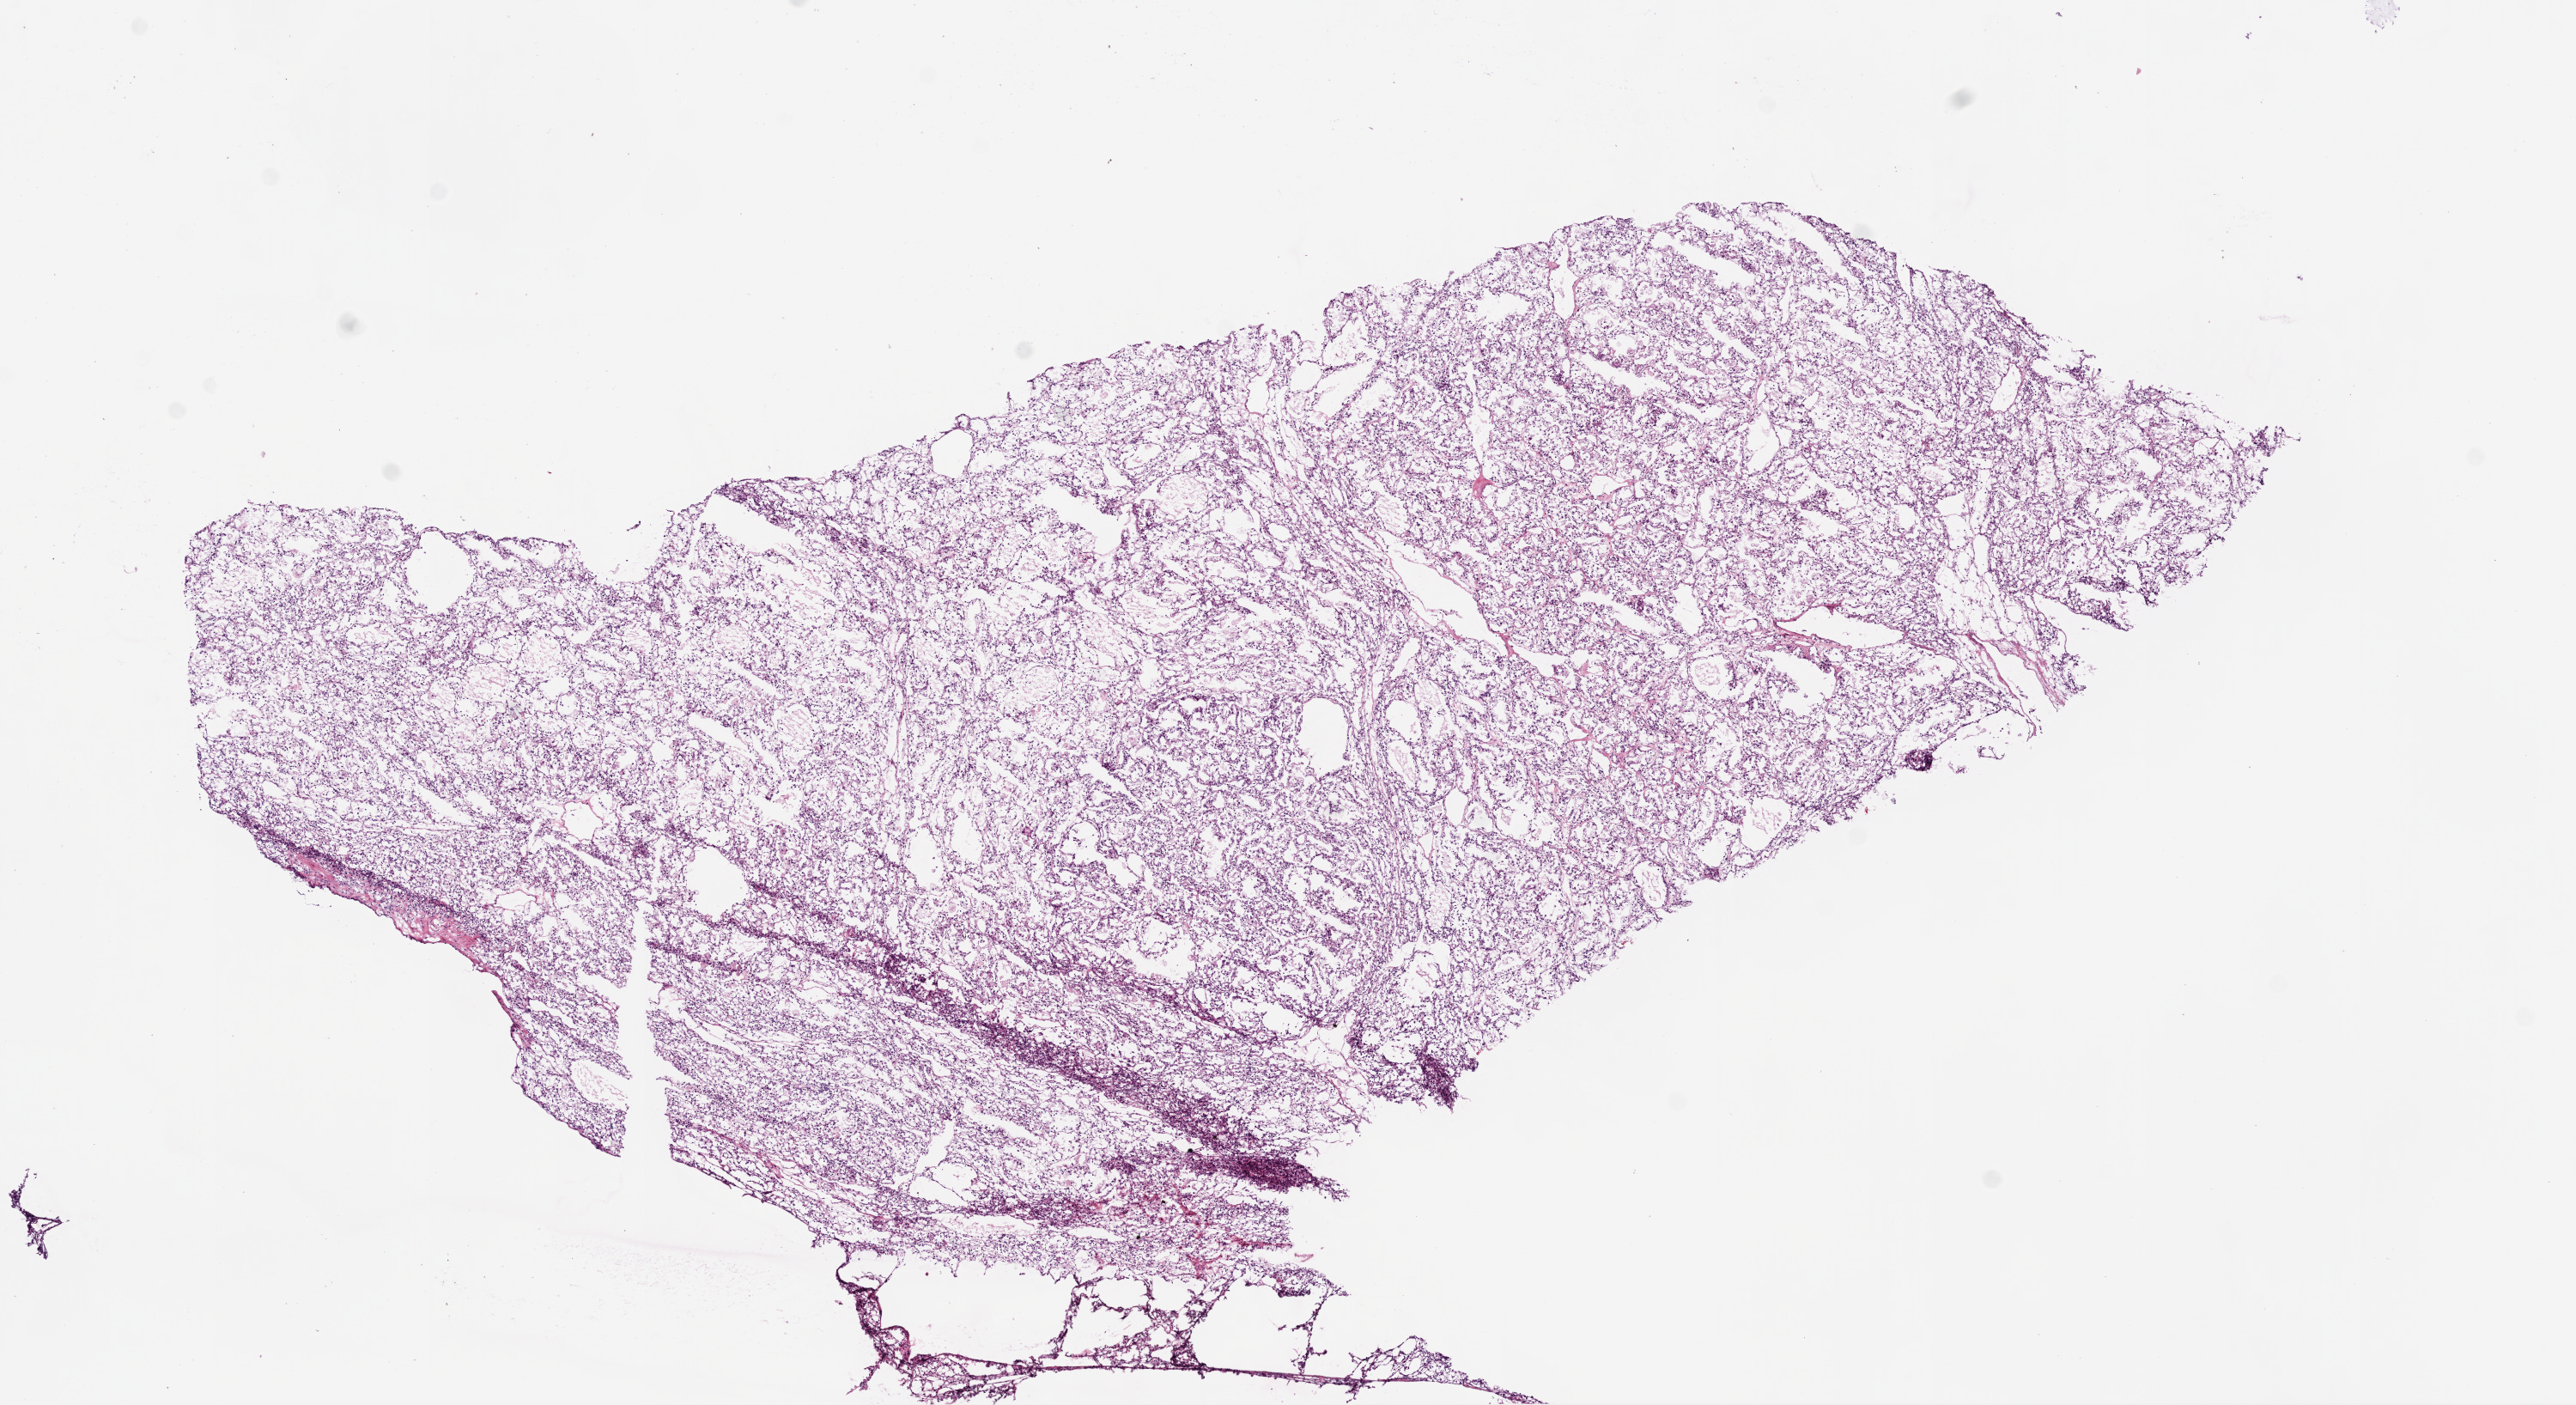
Whole-slide histology image, Hematoxylin and eosin (H&E) stained — whole scanned area (about 12.0 x 6.6 mm) shown as a low-resolution overview, frozen section, kidney, primary tumour sample. Female patient; age at initial diagnosis 51 years. Histologic grade: G3 (poorly differentiated). Slide review estimates, as recorded: tumour cells 90%, tumour nuclei 90%, normal cells 0%, stromal cells 10%, necrosis 0%.
AJCC pathologic stage: III. Diagnosis: Clear cell adenocarcinoma, NOS.